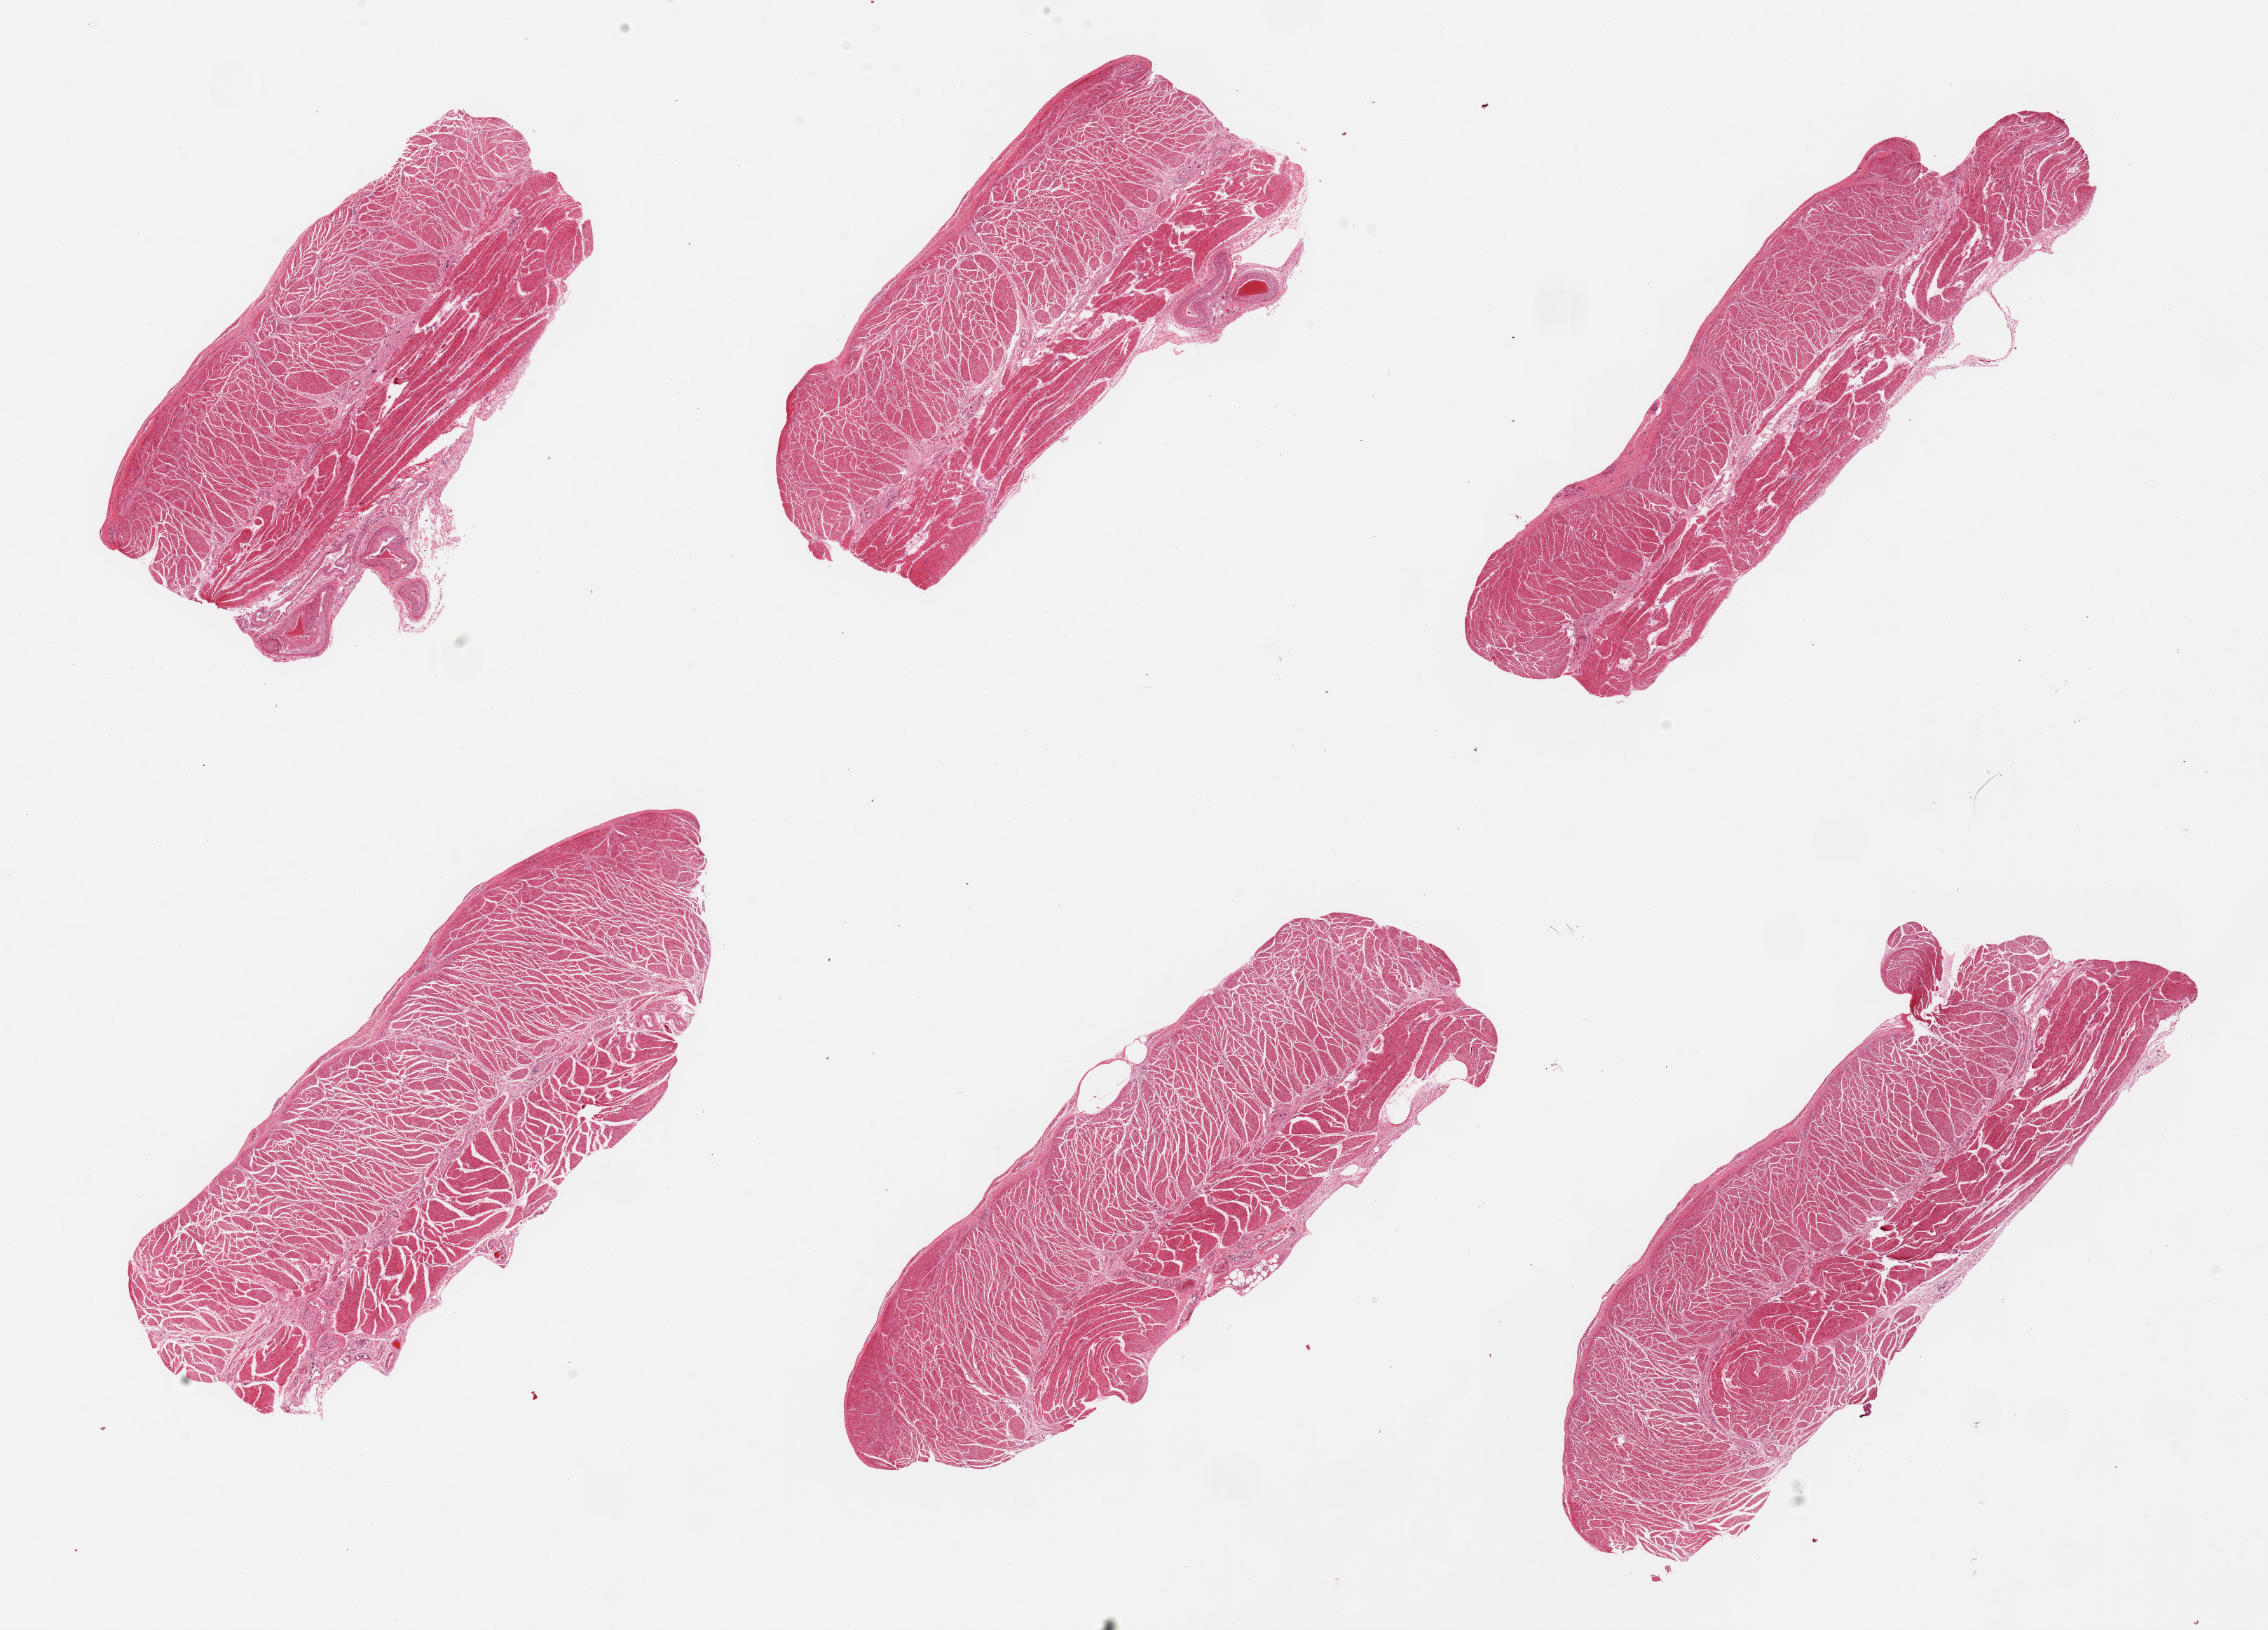
Whole-slide image, H&E stain, low-resolution overview of the scanned area, about 25.6 x 18.4 mm, PAXgene-fixed, paraffin-embedded tissue, section of gastroesophageal junction (target tissue), tissue donor sample. Female donor.
Reviewer comment on this tissue sample: 6 pieces, all muscularis, good specimens.